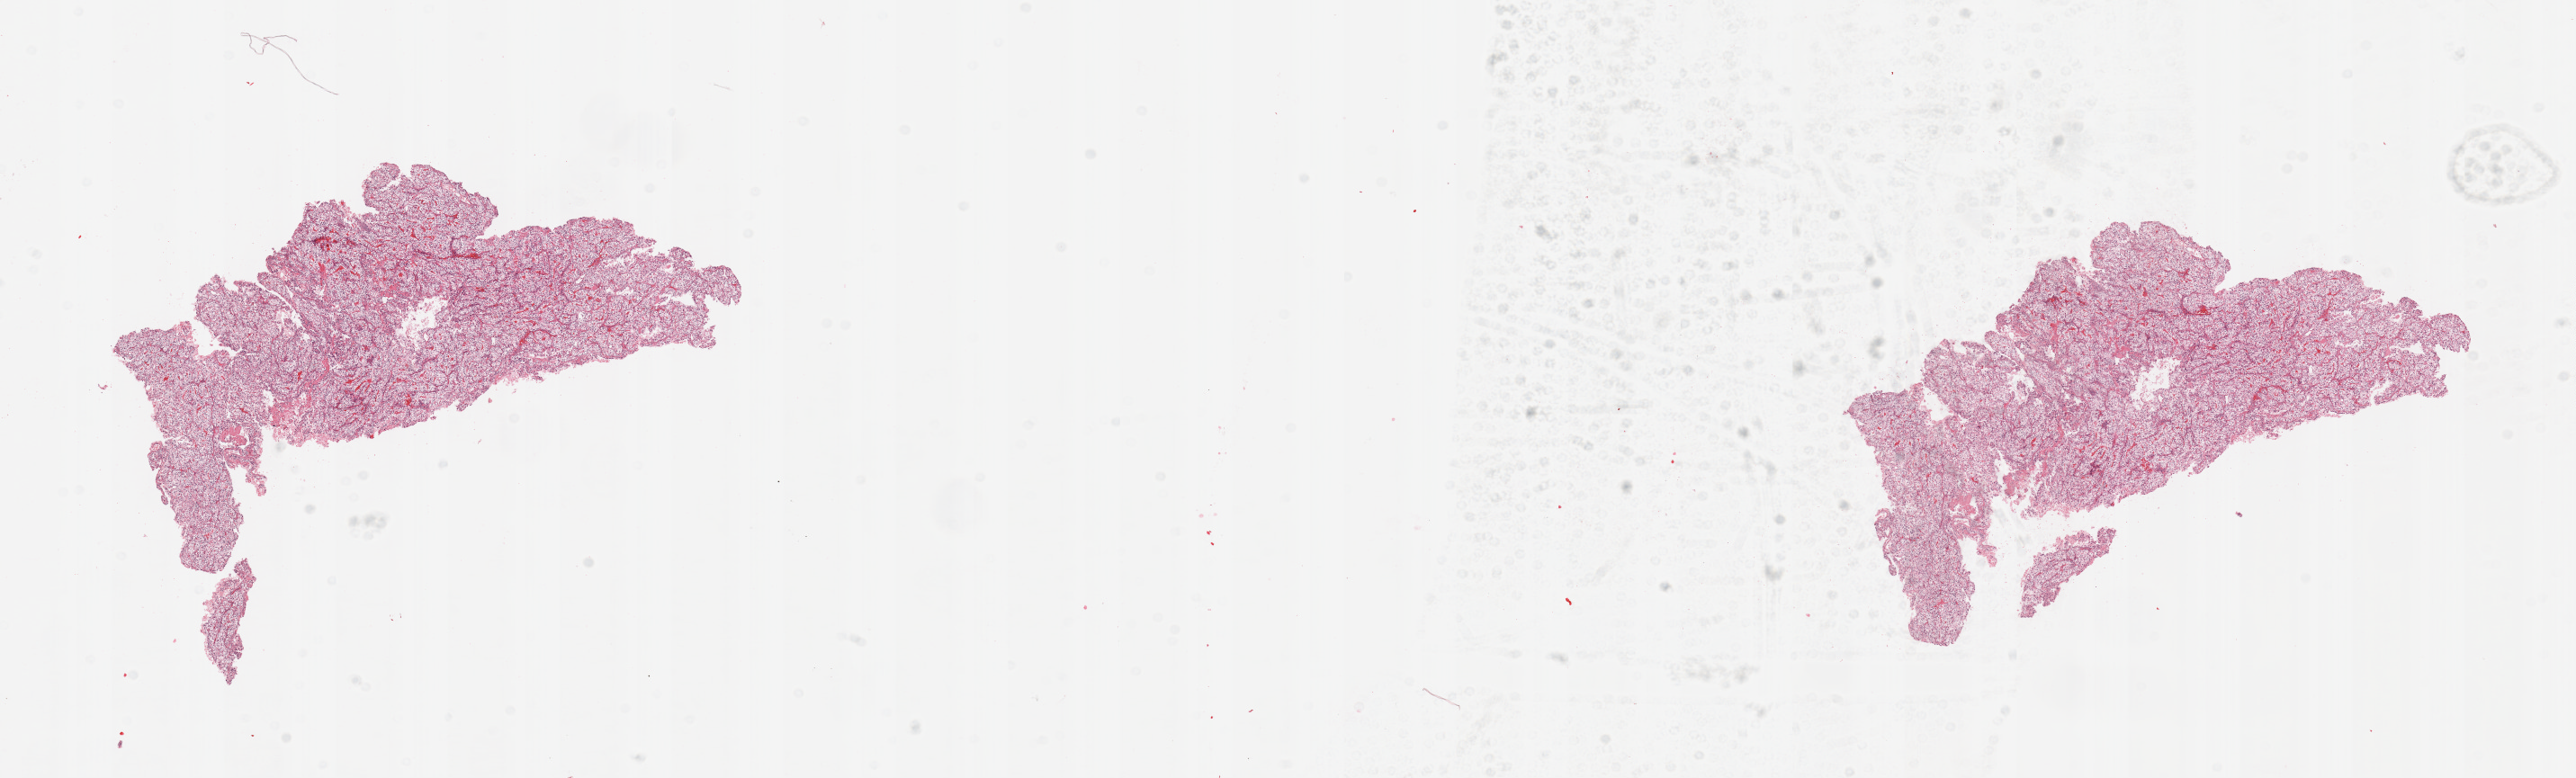
Digitized H&E tissue section (whole slide), a low-resolution overview of the entire scanned area, about 22.6 x 6.8 mm, tumour tissue sample, sampled site: kidney. Patient: male, age 69 years. Histologic grade: G2 (moderately differentiated). Slide review estimates, as recorded: tumour nuclei 95%, necrosis 5%.
• AJCC pathologic stage: I
• diagnosis: Renal cell carcinoma, NOS